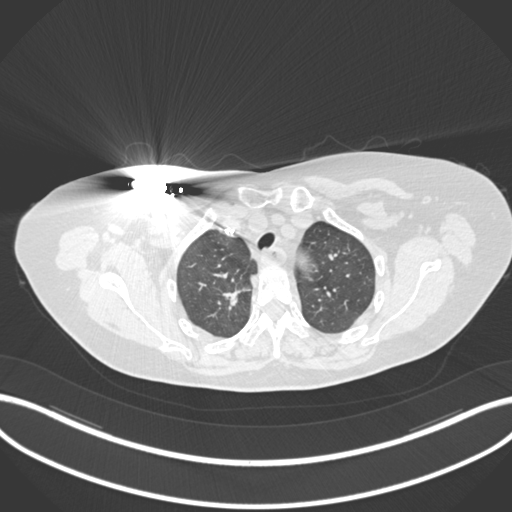
Chest CT, one axial slice. Reconstruction kernel B30f. 120 kVp. Lung window (W 1500 / L -600 HU). 512 × 512 image matrix. Female patient, age 72 years. From the clinical record (not read from this slice): clinical TNM (as recorded): T1c N0 M0.
Annotated regions visible in this slice (bounding box drawn by a radiologist):
- lung tumour (recorded histology: adenocarcinoma): bounding box (x1, y1, x2, y2) in pixels: (216, 279, 250, 311)